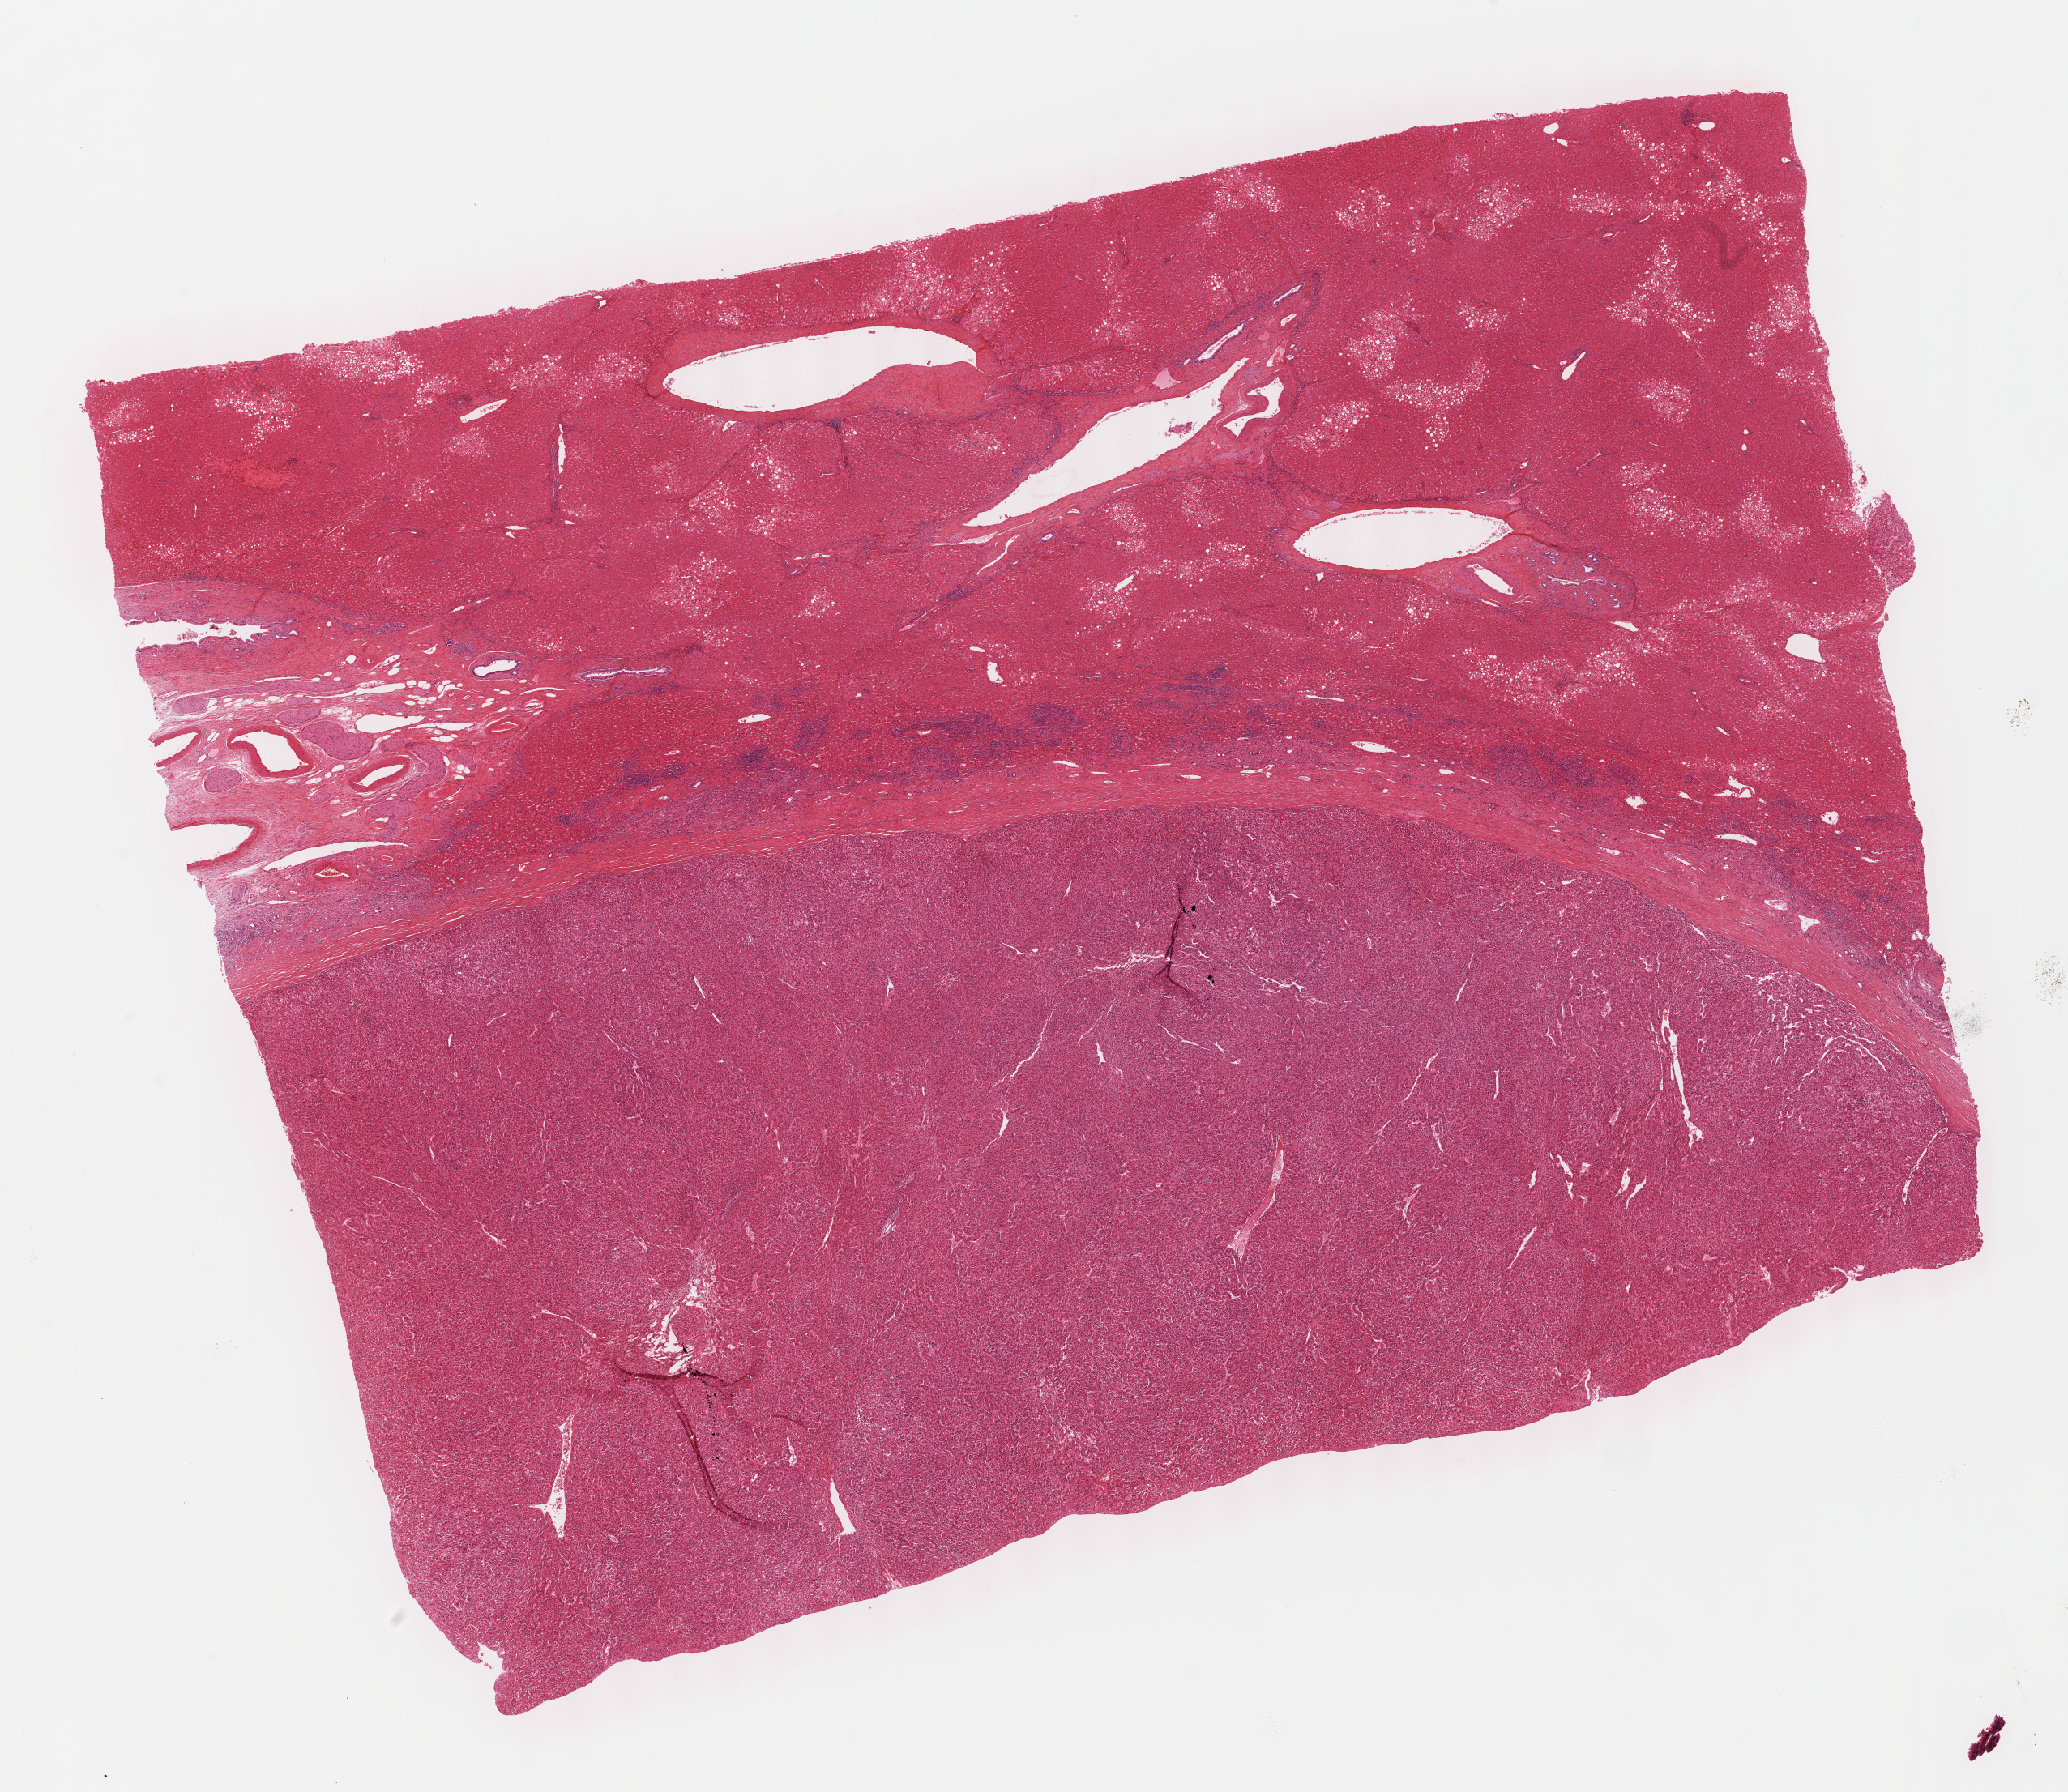
Digitized H&E tissue section (whole slide), low-resolution overview of the scanned area, about 20.6 x 17.9 mm (from a 40x scan); FFPE section; sample: primary tumour, liver. Patient: male, age at initial diagnosis 69 years. Histologic grade: G3 (poorly differentiated).
AJCC pathologic stage: I (7th edition). Pathologic diagnosis: Hepatocellular carcinoma, NOS.